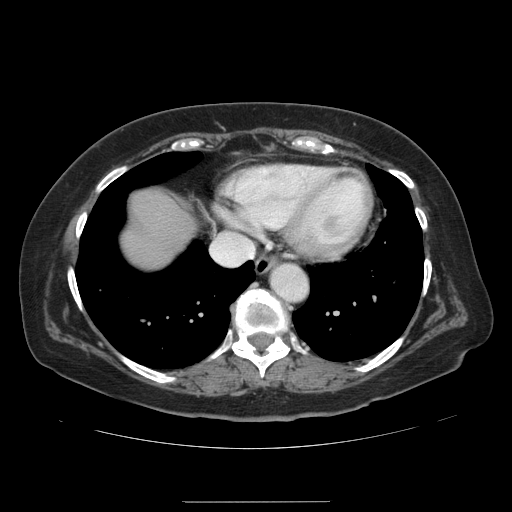
Contrast-enhanced abdominal CT, one axial slice. Slice 127 of 141 in the series (ordered by position). Intravenous contrast given. Soft-tissue window (W 400 / L 40 HU). 2.5 mm slice thickness. 512 × 512 image matrix. Female patient, age 74 years. From the clinical record (not read from this slice): diagnosis: colorectal cancer liver metastases, imaged before liver resection; multiple liver metastases: yes; largest metastasis: 7 cm; chemotherapy before resection: no.
Structures marked on this image (expert manual segmentation):
- hepatic veins: bounding box (x1, y1, x2, y2) in pixels: (222, 233, 242, 237)
- liver: (126, 193, 191, 266)
- planned liver remnant (the part of the liver to remain after resection): (126, 193, 168, 263)